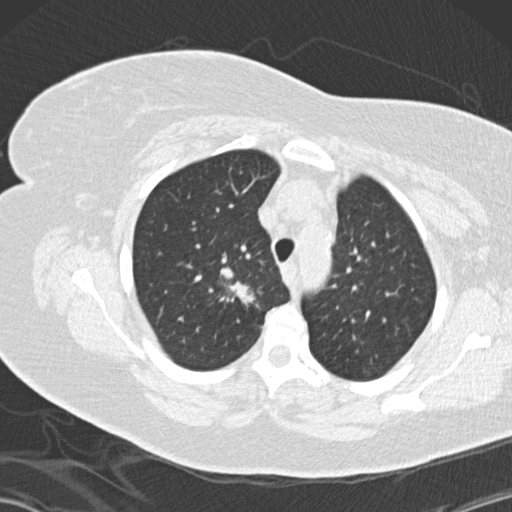
Low-dose screening chest CT, one axial slice; position 113 of 146 along the scan axis; lung window (W 1500 / L -600 HU); 512 × 512 image matrix, field of view 350 × 350 mm.
Outlined on this slice (manually delineated by an expert):
- lesion 1 (tumor, upper lobe of right lung): bounding box <217,268,255,305> (left, top, right, bottom; pixels)